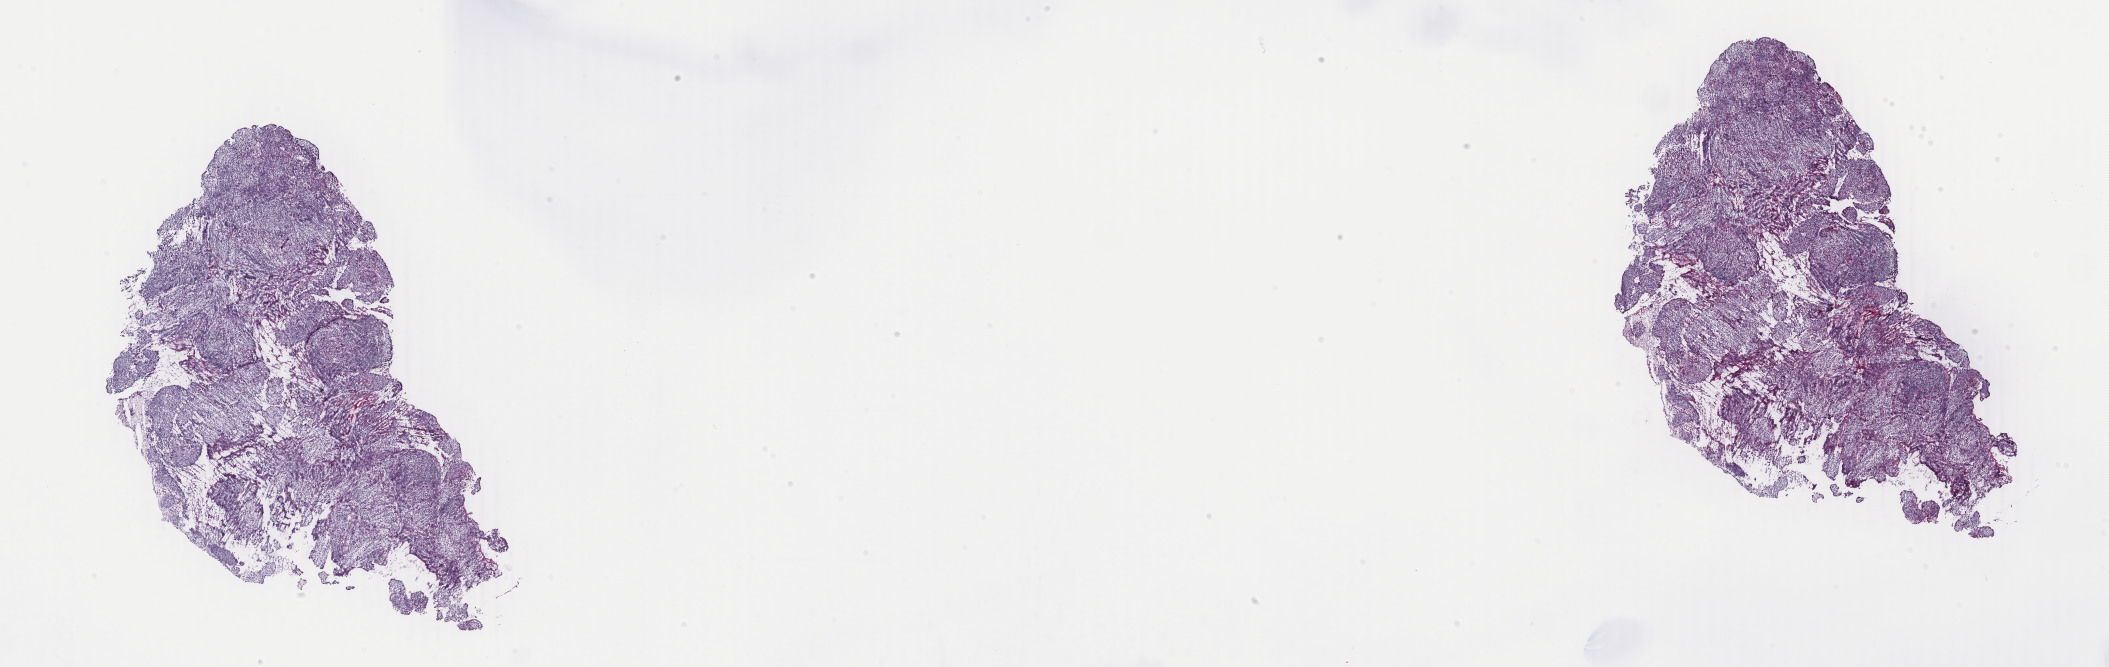
Hematoxylin and eosin (H&E) stained whole-slide image, shown as a low-resolution overview of the whole scanned area (about 33.6 x 10.6 mm, from a 40x scan), frozen section, primary tumour sample from the cervix. Patient: female, age at initial diagnosis 48 years. Composition of this section per pathologist review: tumour cells 90%, tumour nuclei 95%, normal cells 0%, stromal cells 10%, necrosis 0%. Inflammatory infiltration, as recorded: lymphocyte infiltration 0%, monocyte infiltration 0%, neutrophil infiltration 0%.
FIGO stage: IIIB. Diagnosis: Squamous cell carcinoma, large cell, nonkeratinizing, NOS (cervix uteri).